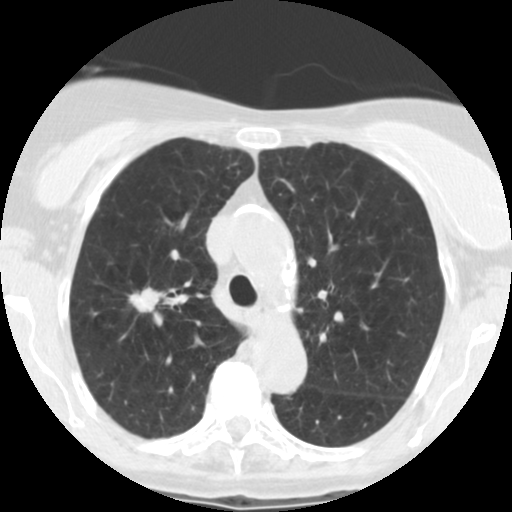
Chest CT (low-dose screening protocol), one axial image. Baseline screening round. Lung window (W 1500 / L -600 HU). Standard (soft-tissue) reconstruction kernel (STANDARD). Female participant, aged 67 years at enrolment. Former smoker at enrolment.
Expert-annotated lung lesion, bounding box <114,279,173,321> (left, top, right, bottom; pixels). The screening reader recorded 6 non-calcified nodules or masses ≥4 mm on this exam; which of them this box marks is not recorded.